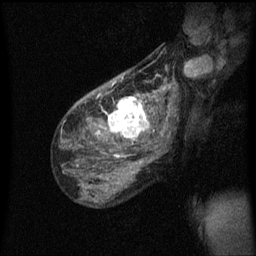
Breast MRI (dynamic contrast-enhanced), one sagittal slice. Slice 37 of 60 in the series (ordered by position). Dynamic contrast-enhanced series, image 2 of 3 at this slice position (ordered by acquisition). 1.5 T. TE 4.2 ms, TR 8.4 ms. 256 × 256 image matrix. Female patient, age 49 years.
Structures marked on this image (semi-automatic segmentation, software-assisted and operator-edited):
- analysis volume of interest (the breast-tissue region the enhancement analysis was run in; not a lesion): bounding box [x1, y1, x2, y2] px = [103, 90, 157, 151]
- tumour enhancement mask (voxels above the 70 % enhancement threshold inside the analysis volume of interest): [105, 96, 150, 141]